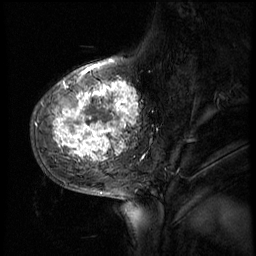
Breast MRI (dynamic contrast-enhanced), one sagittal slice; position 17 of 56 along the scan axis; 4 images stored at this slice position (order not interpretable as contrast timing); 1.5 T; TE 4.2 ms, TR 8.9 ms; 2.5 mm slice thickness; 256 × 256 image matrix, field of view 220 × 220 mm. Patient: female, 51 years. Case-level facts recorded for this patient, not image findings: setting: breast cancer imaged before/during neoadjuvant chemotherapy; receptor status: triple-negative.
Structures marked on this image (semi-automatic segmentation, software-assisted and operator-edited):
- analysis volume of interest (the breast-tissue region the enhancement analysis was run in; not a lesion): bounding box <31,70,150,173> (left, top, right, bottom; pixels)
- tumour enhancement mask (voxels above the 140 % enhancement threshold inside the analysis volume of interest): <55,70,138,161>